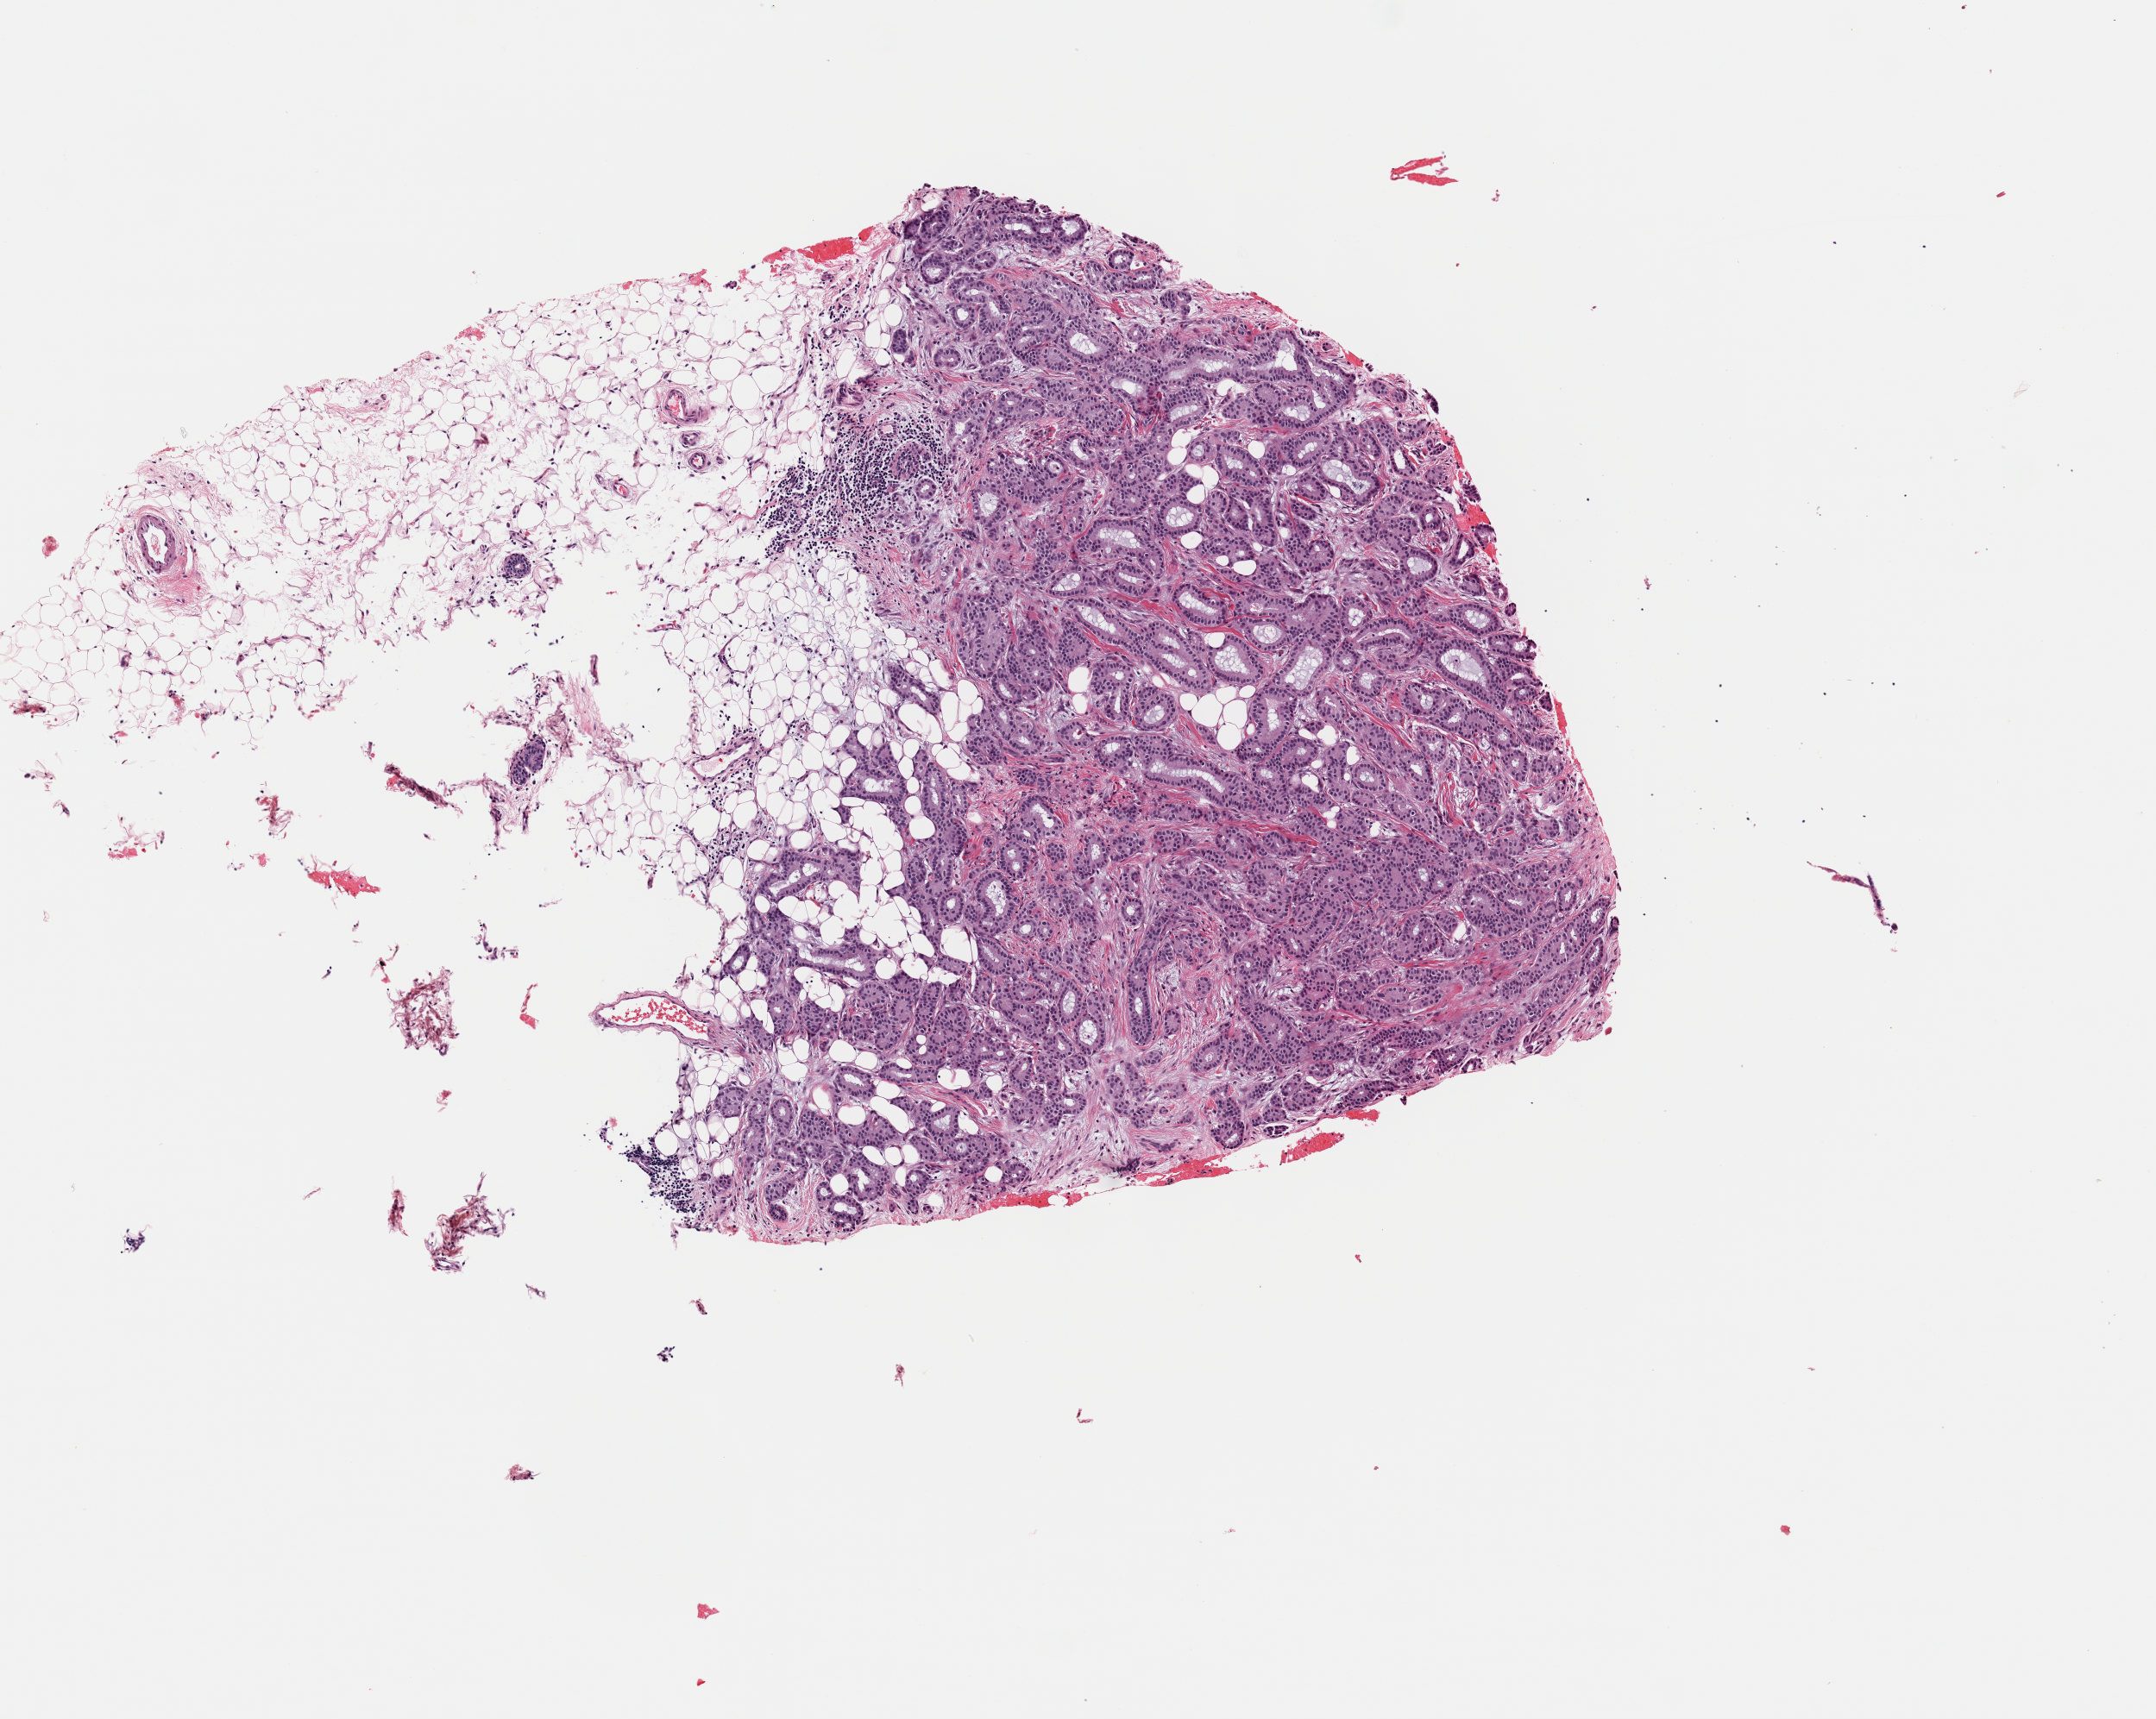
Whole-slide histology image, Hematoxylin and eosin (H&E) stained, shown as a low-resolution overview of the whole scanned area (about 4.9 x 3.9 mm); frozen section; breast, primary tumour sample. Female, age 79 years at initial diagnosis. Slide review estimates, as recorded: tumour cells 45%, tumour nuclei 80%, normal cells 5%, stromal cells 50%, necrosis 0%. Inflammatory infiltration, as recorded: lymphocyte infiltration 1%, monocyte infiltration 0%, neutrophil infiltration 0%.
AJCC pathologic stage: IIA (7th edition). Diagnosis: Infiltrating duct carcinoma, NOS. Laterality: left.